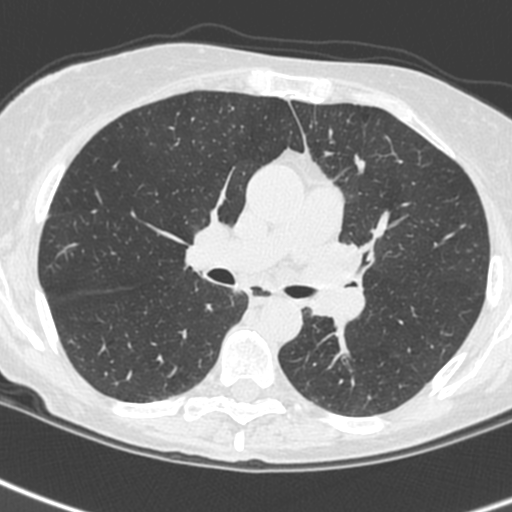
Low-dose screening chest CT, one axial slice. Position 147 of 242 along the scan axis. 120 kVp. Lung window (W 1500 / L -600 HU). 512 × 512 image matrix, field of view 284 × 284 mm.
Outlined on this slice (expert manual segmentation):
- lesion 3 (tumor, upper lobe of left lung): bounding box (x1, y1, x2, y2) in pixels: (307, 241, 365, 326)